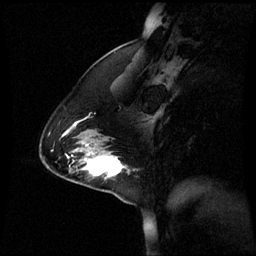
Breast MRI (dynamic contrast-enhanced), one sagittal slice. Slice 19 of 60 in the series (ordered by position). Dynamic contrast-enhanced series, image 2 of 3 at this slice position (ordered by acquisition). 1.5 T. TE 4.2 ms, TR 8.9 ms. 256 × 256 image matrix, field of view 240 × 240 mm. Patient: female, 44 years. From the clinical record (not read from this slice): setting: breast cancer imaged before/during neoadjuvant chemotherapy; receptor status: triple-negative.
Outlined on this slice (semi-automatically segmented with operator editing):
- analysis volume of interest (the breast-tissue region the enhancement analysis was run in; not a lesion): box from (x=76, y=150) to (x=129, y=185) px
- tumour enhancement mask (voxels above the 70 % enhancement threshold inside the analysis volume of interest): (x=84, y=156)–(x=123, y=177)